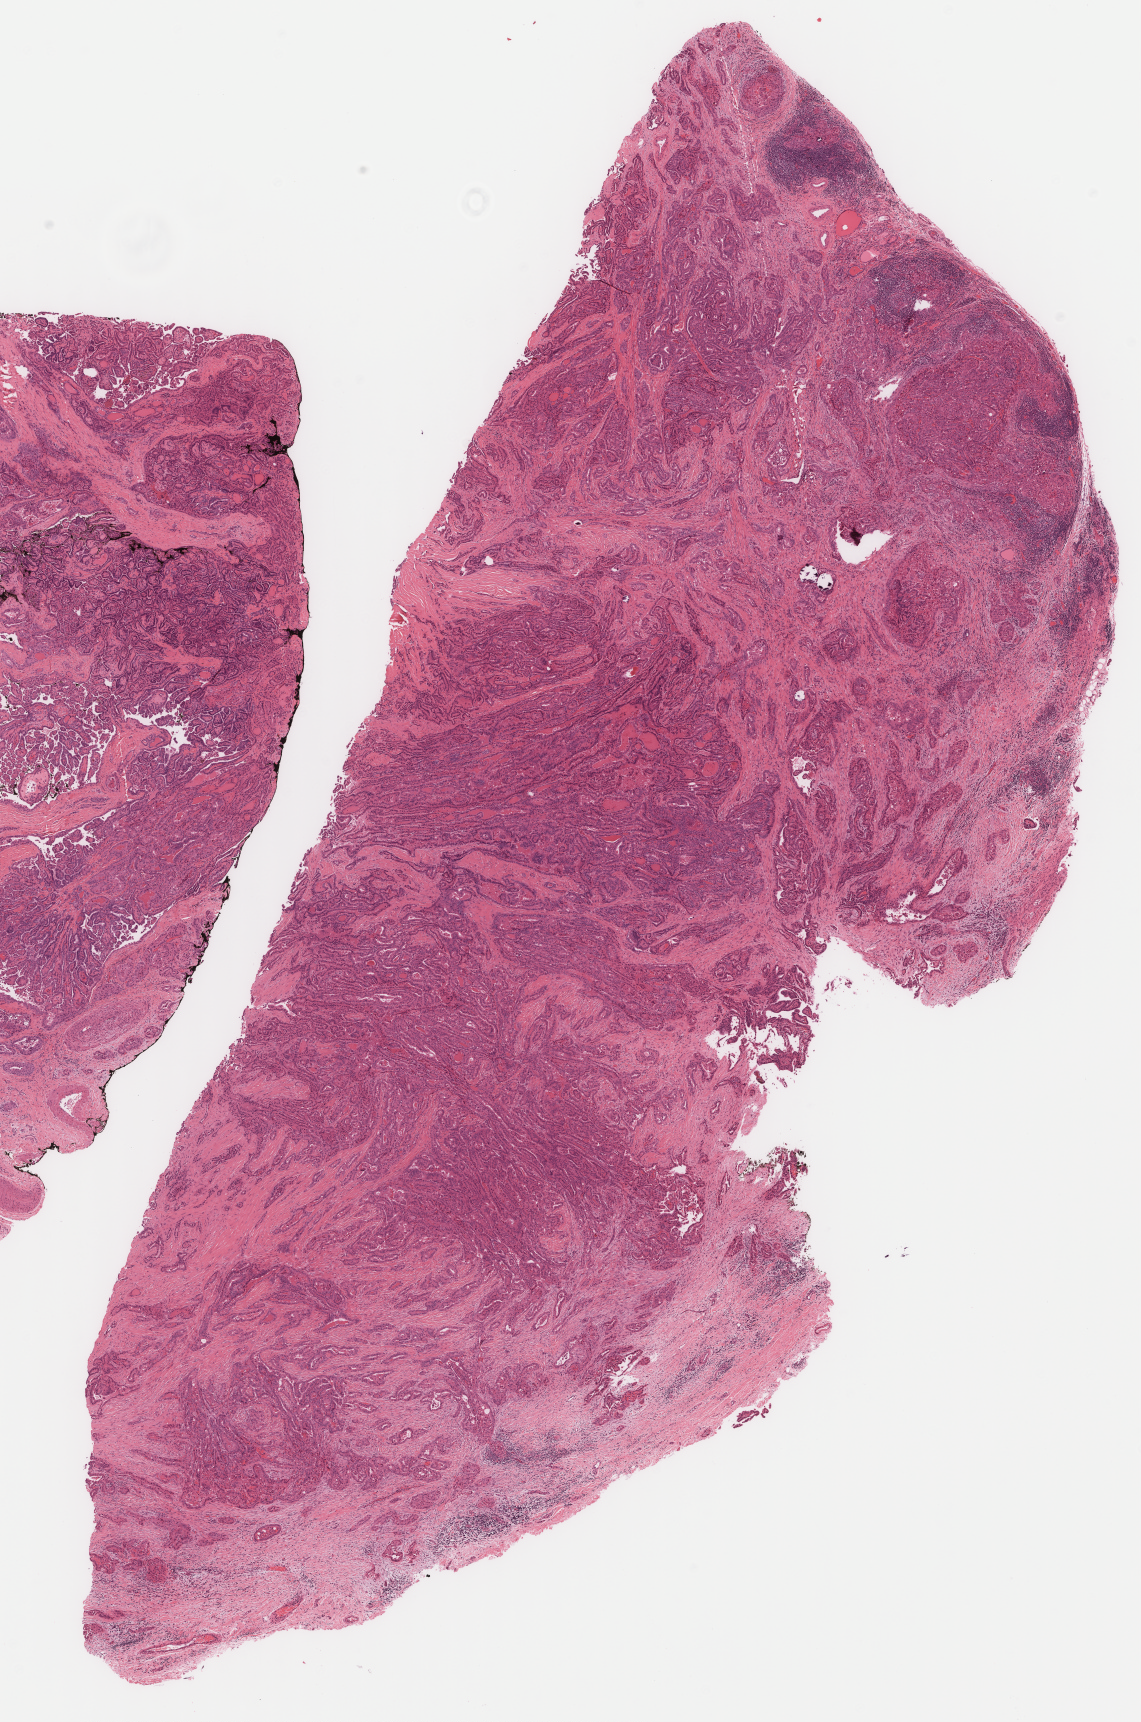
H&E-stained whole-slide image — shown as a low-resolution overview of the whole scanned area (about 9.2 x 13.9 mm, from a 40x scan), formalin-fixed paraffin-embedded (FFPE) diagnostic section, primary tumour sample from the thyroid. Male patient; age at initial diagnosis 57 years.
AJCC pathologic stage: IVA. Pathologic diagnosis: Papillary adenocarcinoma, NOS (thyroid gland). TNM: T2 N1b MX.